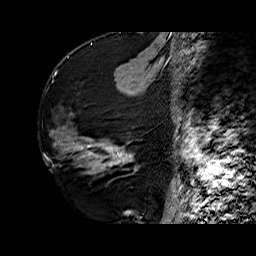
Breast MRI (dynamic contrast-enhanced), one sagittal slice. Position 25 of 60 along the scan axis. Dynamic contrast-enhanced series, time point 2 of 6 at this slice position (early post-contrast). 1.5 T. TE 6.4 ms, TR 32.7 ms. 4 mm slice thickness. 256 × 256 image matrix. Female patient. Case-level facts recorded for this patient, not image findings: setting: breast cancer imaged before/during neoadjuvant chemotherapy; receptor status: HR-positive, HER2-negative.
Annotated regions visible in this slice (semi-automatic segmentation, software-assisted and operator-edited):
- analysis volume of interest (the breast-tissue region the enhancement analysis was run in; not a lesion): bounding box <73,129,141,175> (left, top, right, bottom; pixels)
- tumour enhancement mask (voxels above the 100 % enhancement threshold inside the analysis volume of interest): <87,144,131,163>